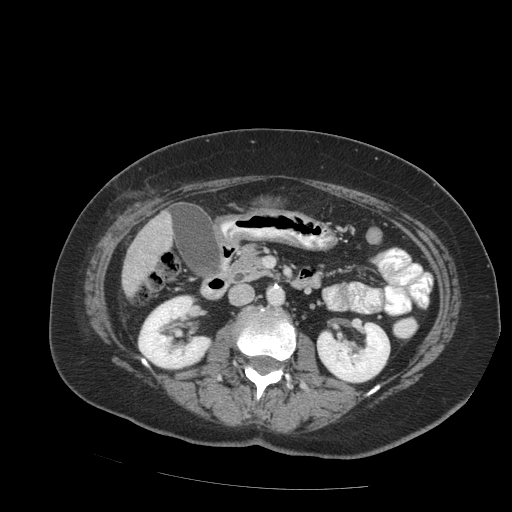
Contrast-enhanced abdominal CT (liver protocol), one axial slice. Soft-tissue window (W 400 / L 40 HU). 2.5 mm slice thickness. 512 × 512 image matrix. Case-level facts recorded for this patient, not image findings: diagnosis: hepatocellular carcinoma (patient treated with transarterial chemoembolisation; whether this scan precedes or follows treatment is not stated here); TNM stage (as recorded): Stage-IVB; Child-Pugh class: A; tumour nodularity: uninodular.
Structures marked on this image (semi-automatically segmented with operator editing):
- liver parenchyma outside the tumour (the mass and vessels are separate outlines, so this box may not span the whole liver): box from (x=122, y=212) to (x=172, y=296) px